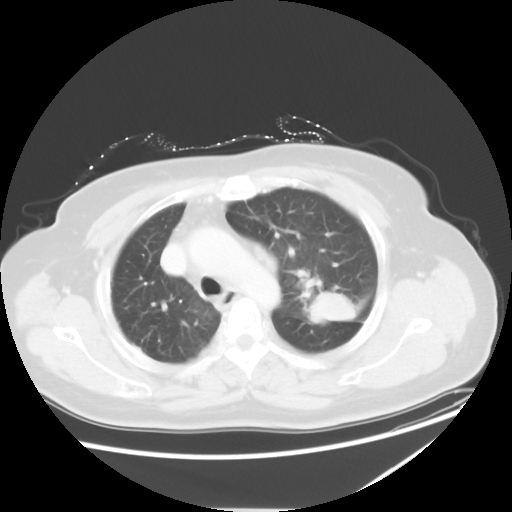
Chest CT, one axial slice. Slice 40 of 54 in the series (ordered by position). Lung window (W 1500 / L -600 HU). 5 mm slice thickness. 512 × 512 image matrix, field of view 384 × 384 mm. Patient: female, 61 years. From the clinical record (not read from this slice): clinical TNM (as recorded): T1c N3 M1.
Outlined on this slice (rectangle marked by the reading radiologist):
- lung tumour (recorded histology: adenocarcinoma): bounding box (x1, y1, x2, y2) in pixels: (301, 287, 363, 332)